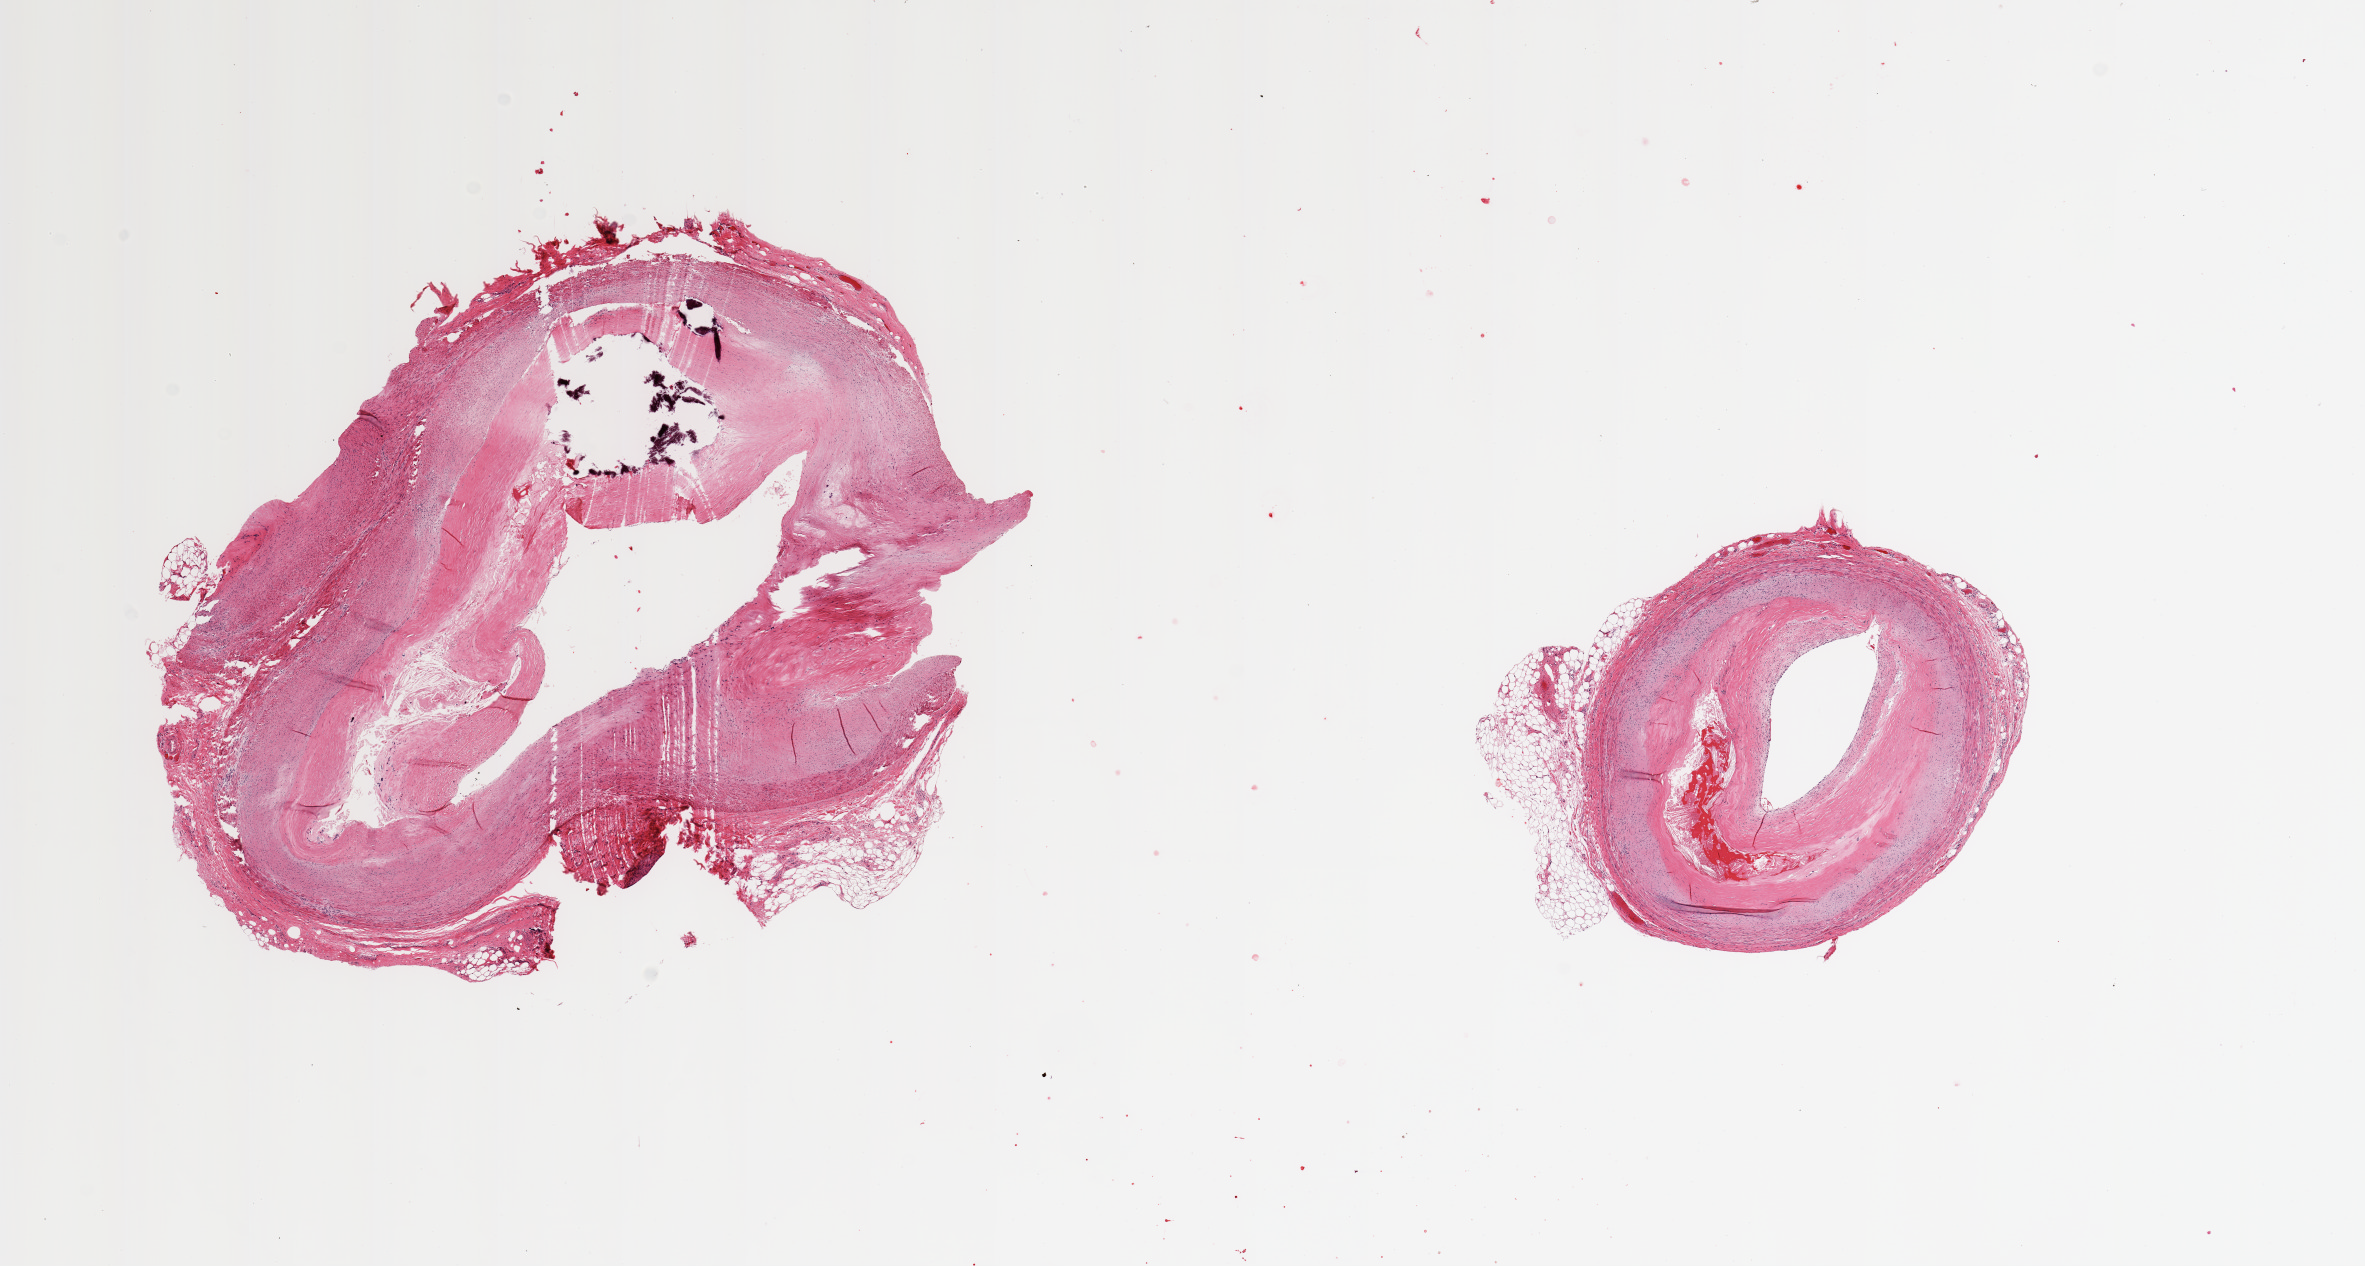
Whole-slide image, hematoxylin and eosin (H&E) stain, a low-resolution overview of the entire scanned area, about 18.7 x 10.0 mm (acquisition: 20x scan); PAXgene-fixed paraffin-embedded (PFPE) section; sampled site (target tissue): coronary artery; donor tissue sample.
Reviewer comment on this tissue sample: 2 pieces; severe calcific atherosclerosis with hemorrhage within plaque and narrowing of the lumen.